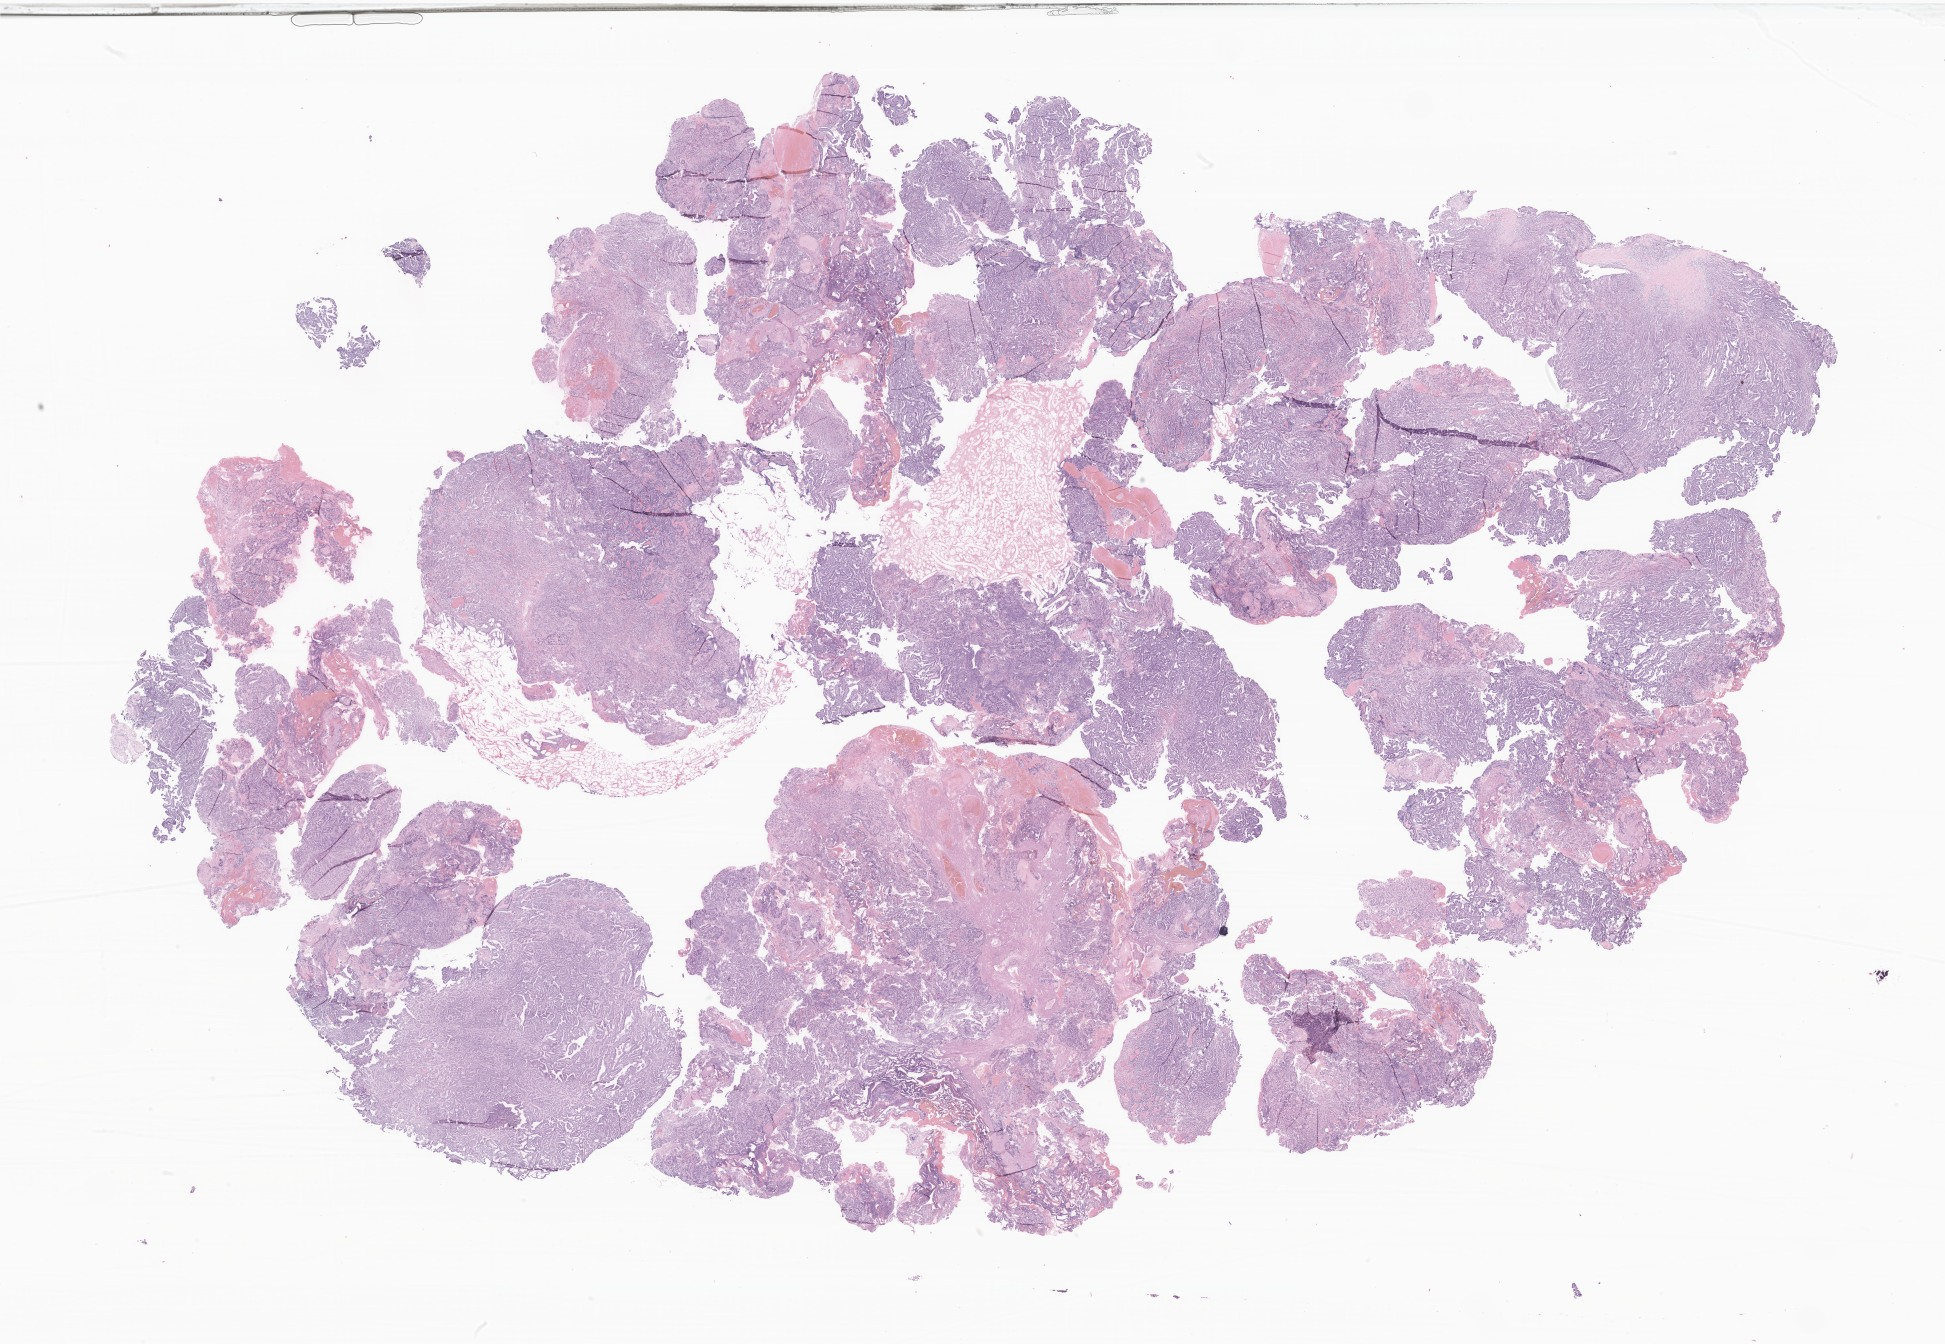
Whole-slide image, hematoxylin and eosin (H&E) stain of tumor tissue from the brain — whole scanned area (about 32.8 x 22.7 mm) shown as a low-resolution overview, formalin-fixed paraffin-embedded section. Patient female; age 51 months (4 years 3 months).
Diagnosis (ICD-O-3 morphology term): Atypical choroid plexus papilloma.